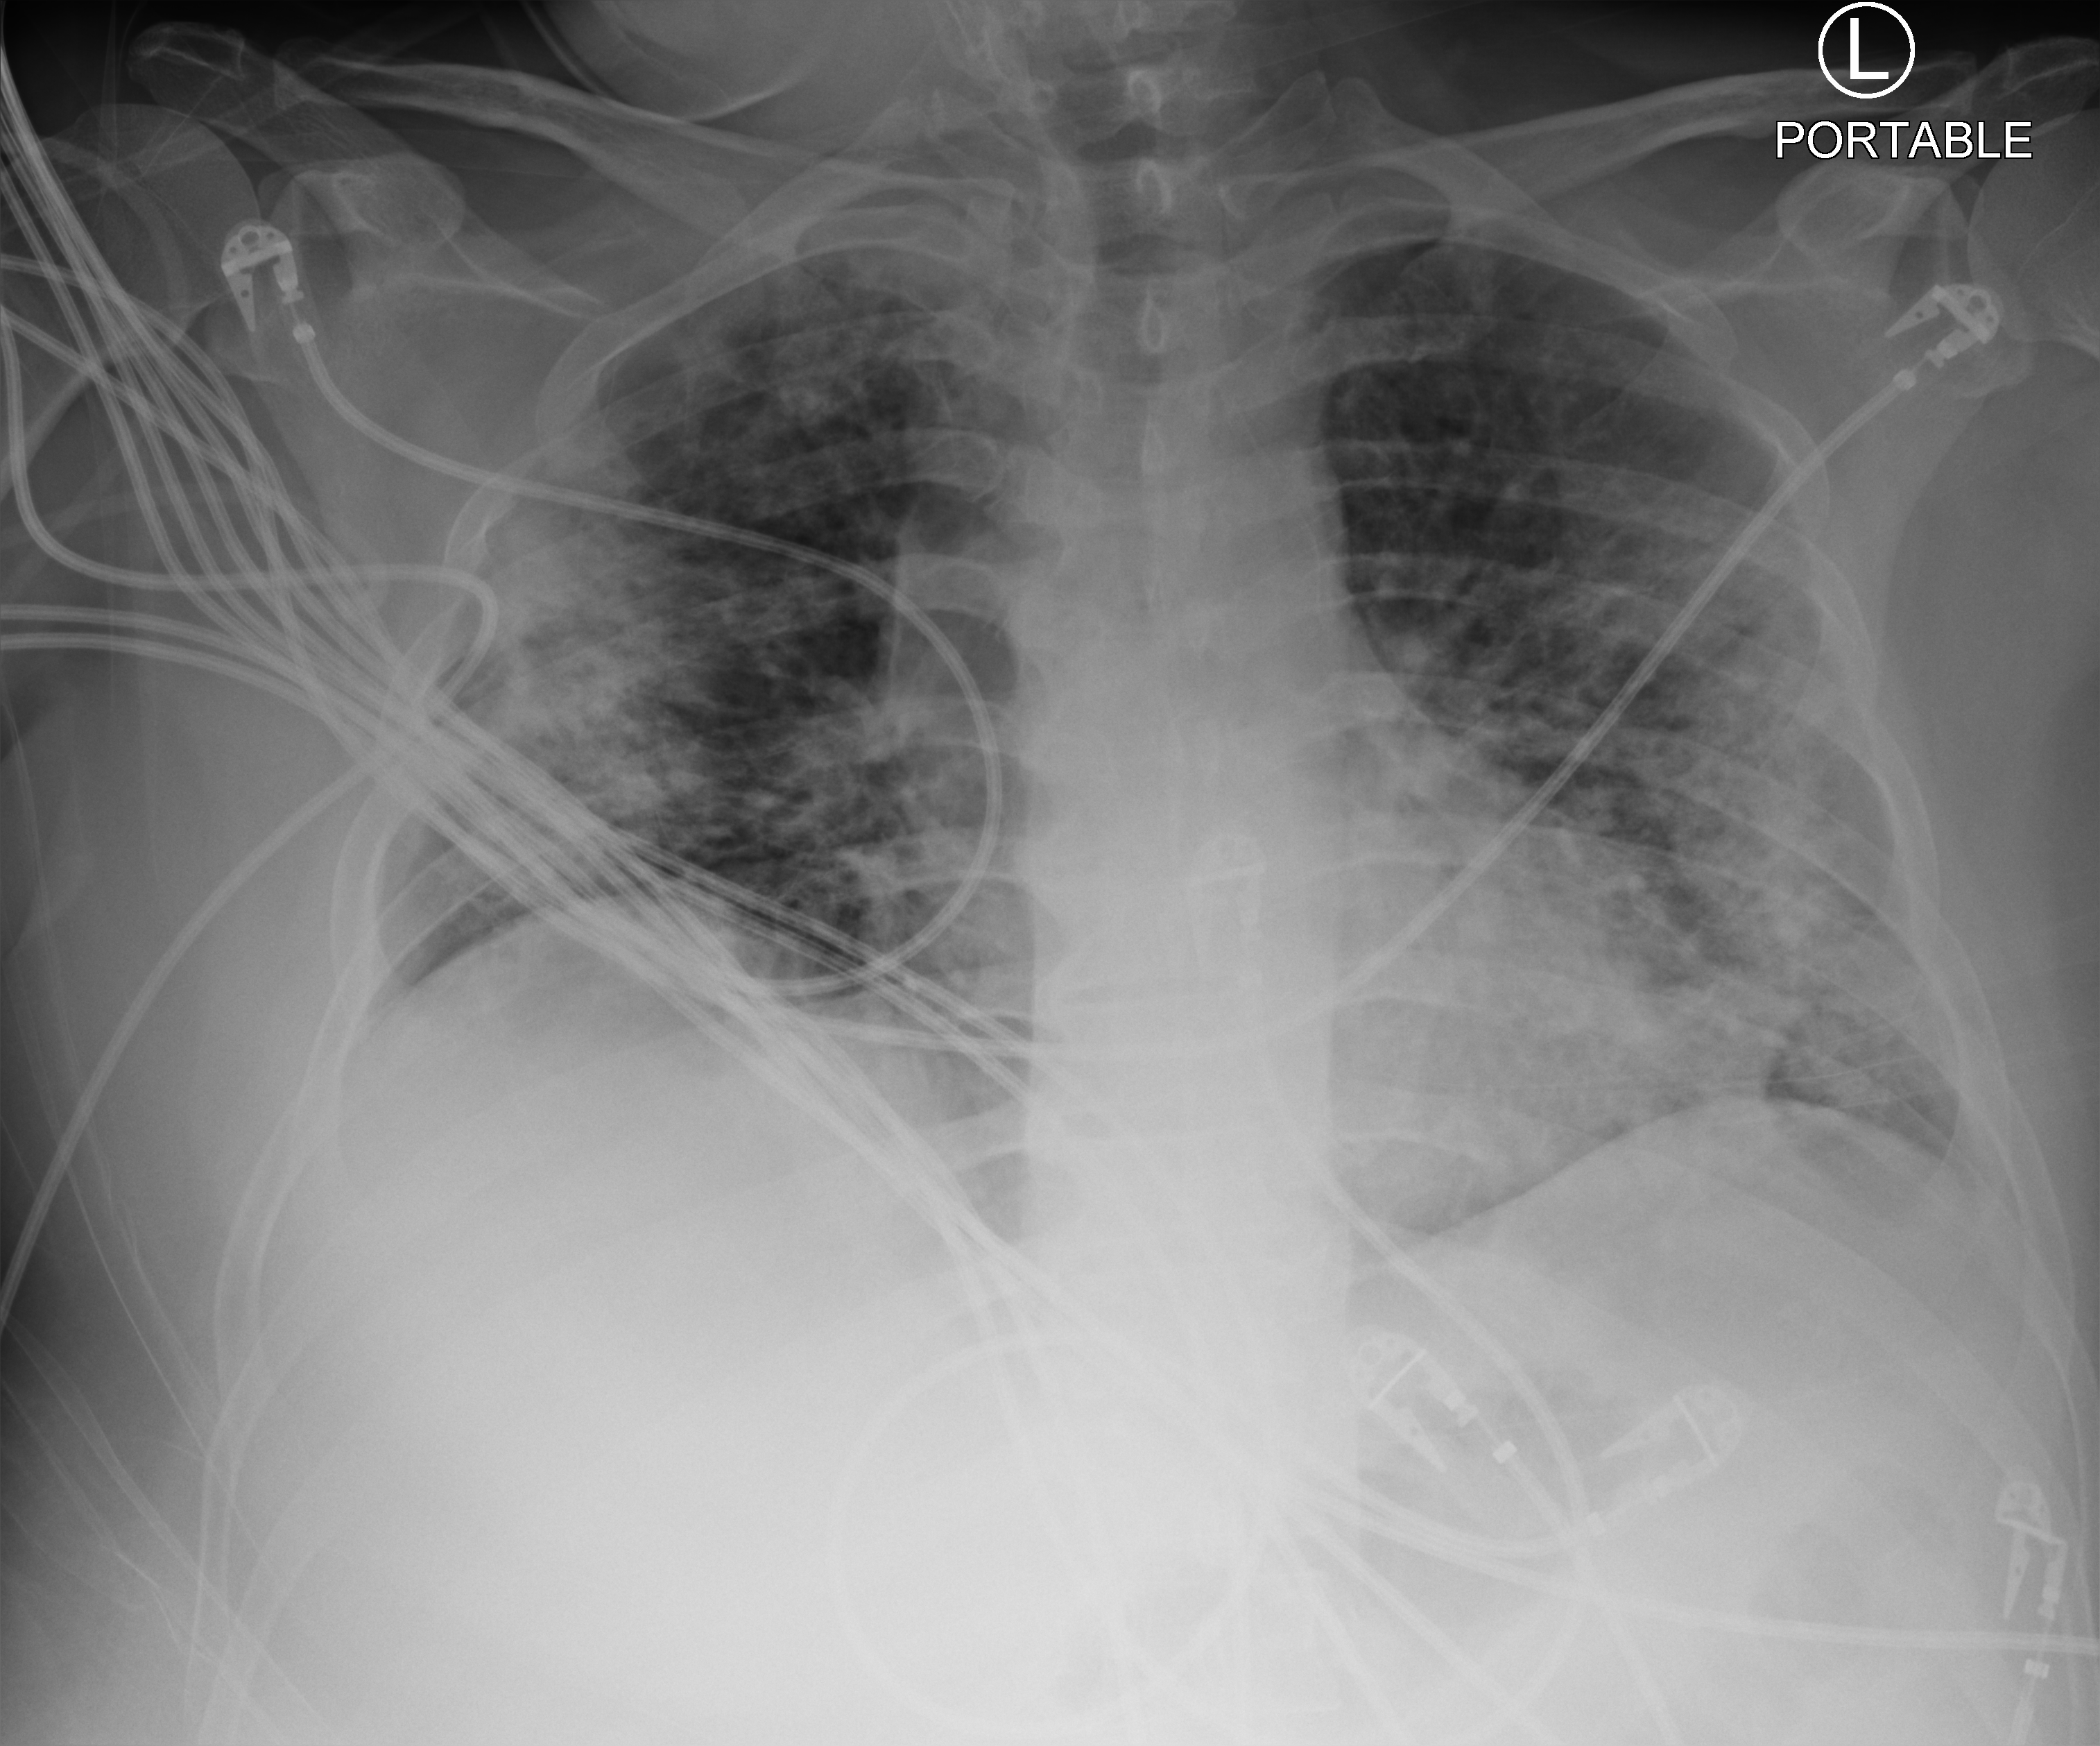
Chest X-ray (portable). Male patient hospitalised with COVID-19, age 18–59 years.
From the hospital-stay record, not from the radiograph (when in the stay this image was taken is not recorded): length of hospital stay: 24 days; admitted to intensive care during this hospital stay: yes; chronic kidney disease (admission record): no.